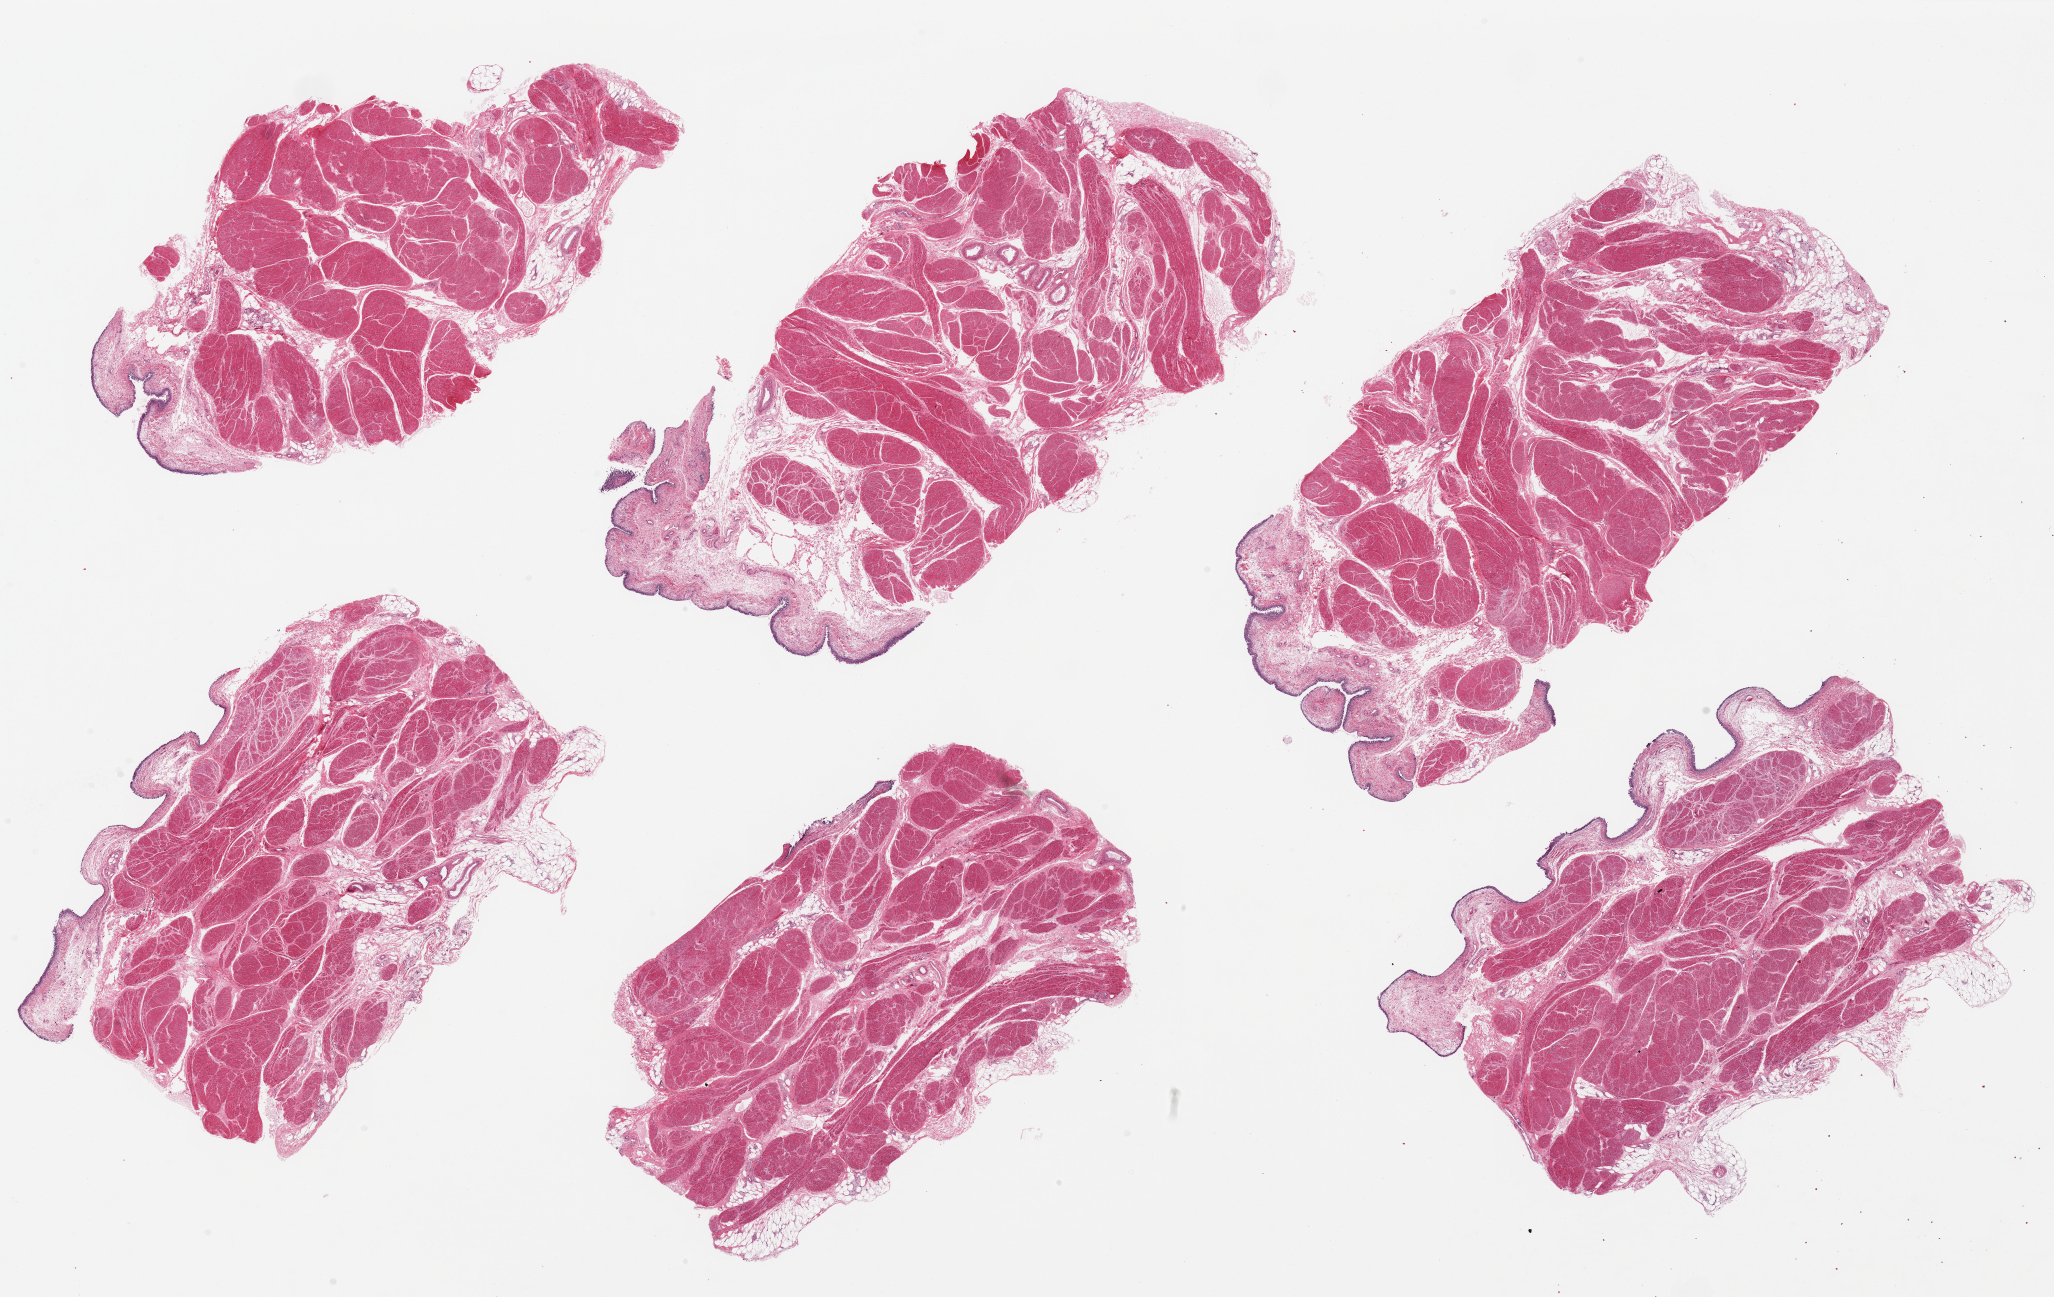
Whole-slide image, H&E stain, brightfield — a low-resolution overview of the entire scanned area, about 32.5 x 20.5 mm (slide scanned at 20x). PAXgene-fixed, paraffin-embedded tissue. Section of urinary bladder (target tissue). Donor tissue sample. Donor sex: male.
Pathologist's review note for this sample: 1 (muscle)-3(urothelium); 6 9.5x6mm pieces; urothelium totally sloughed in places; where present, <1% of thickness.